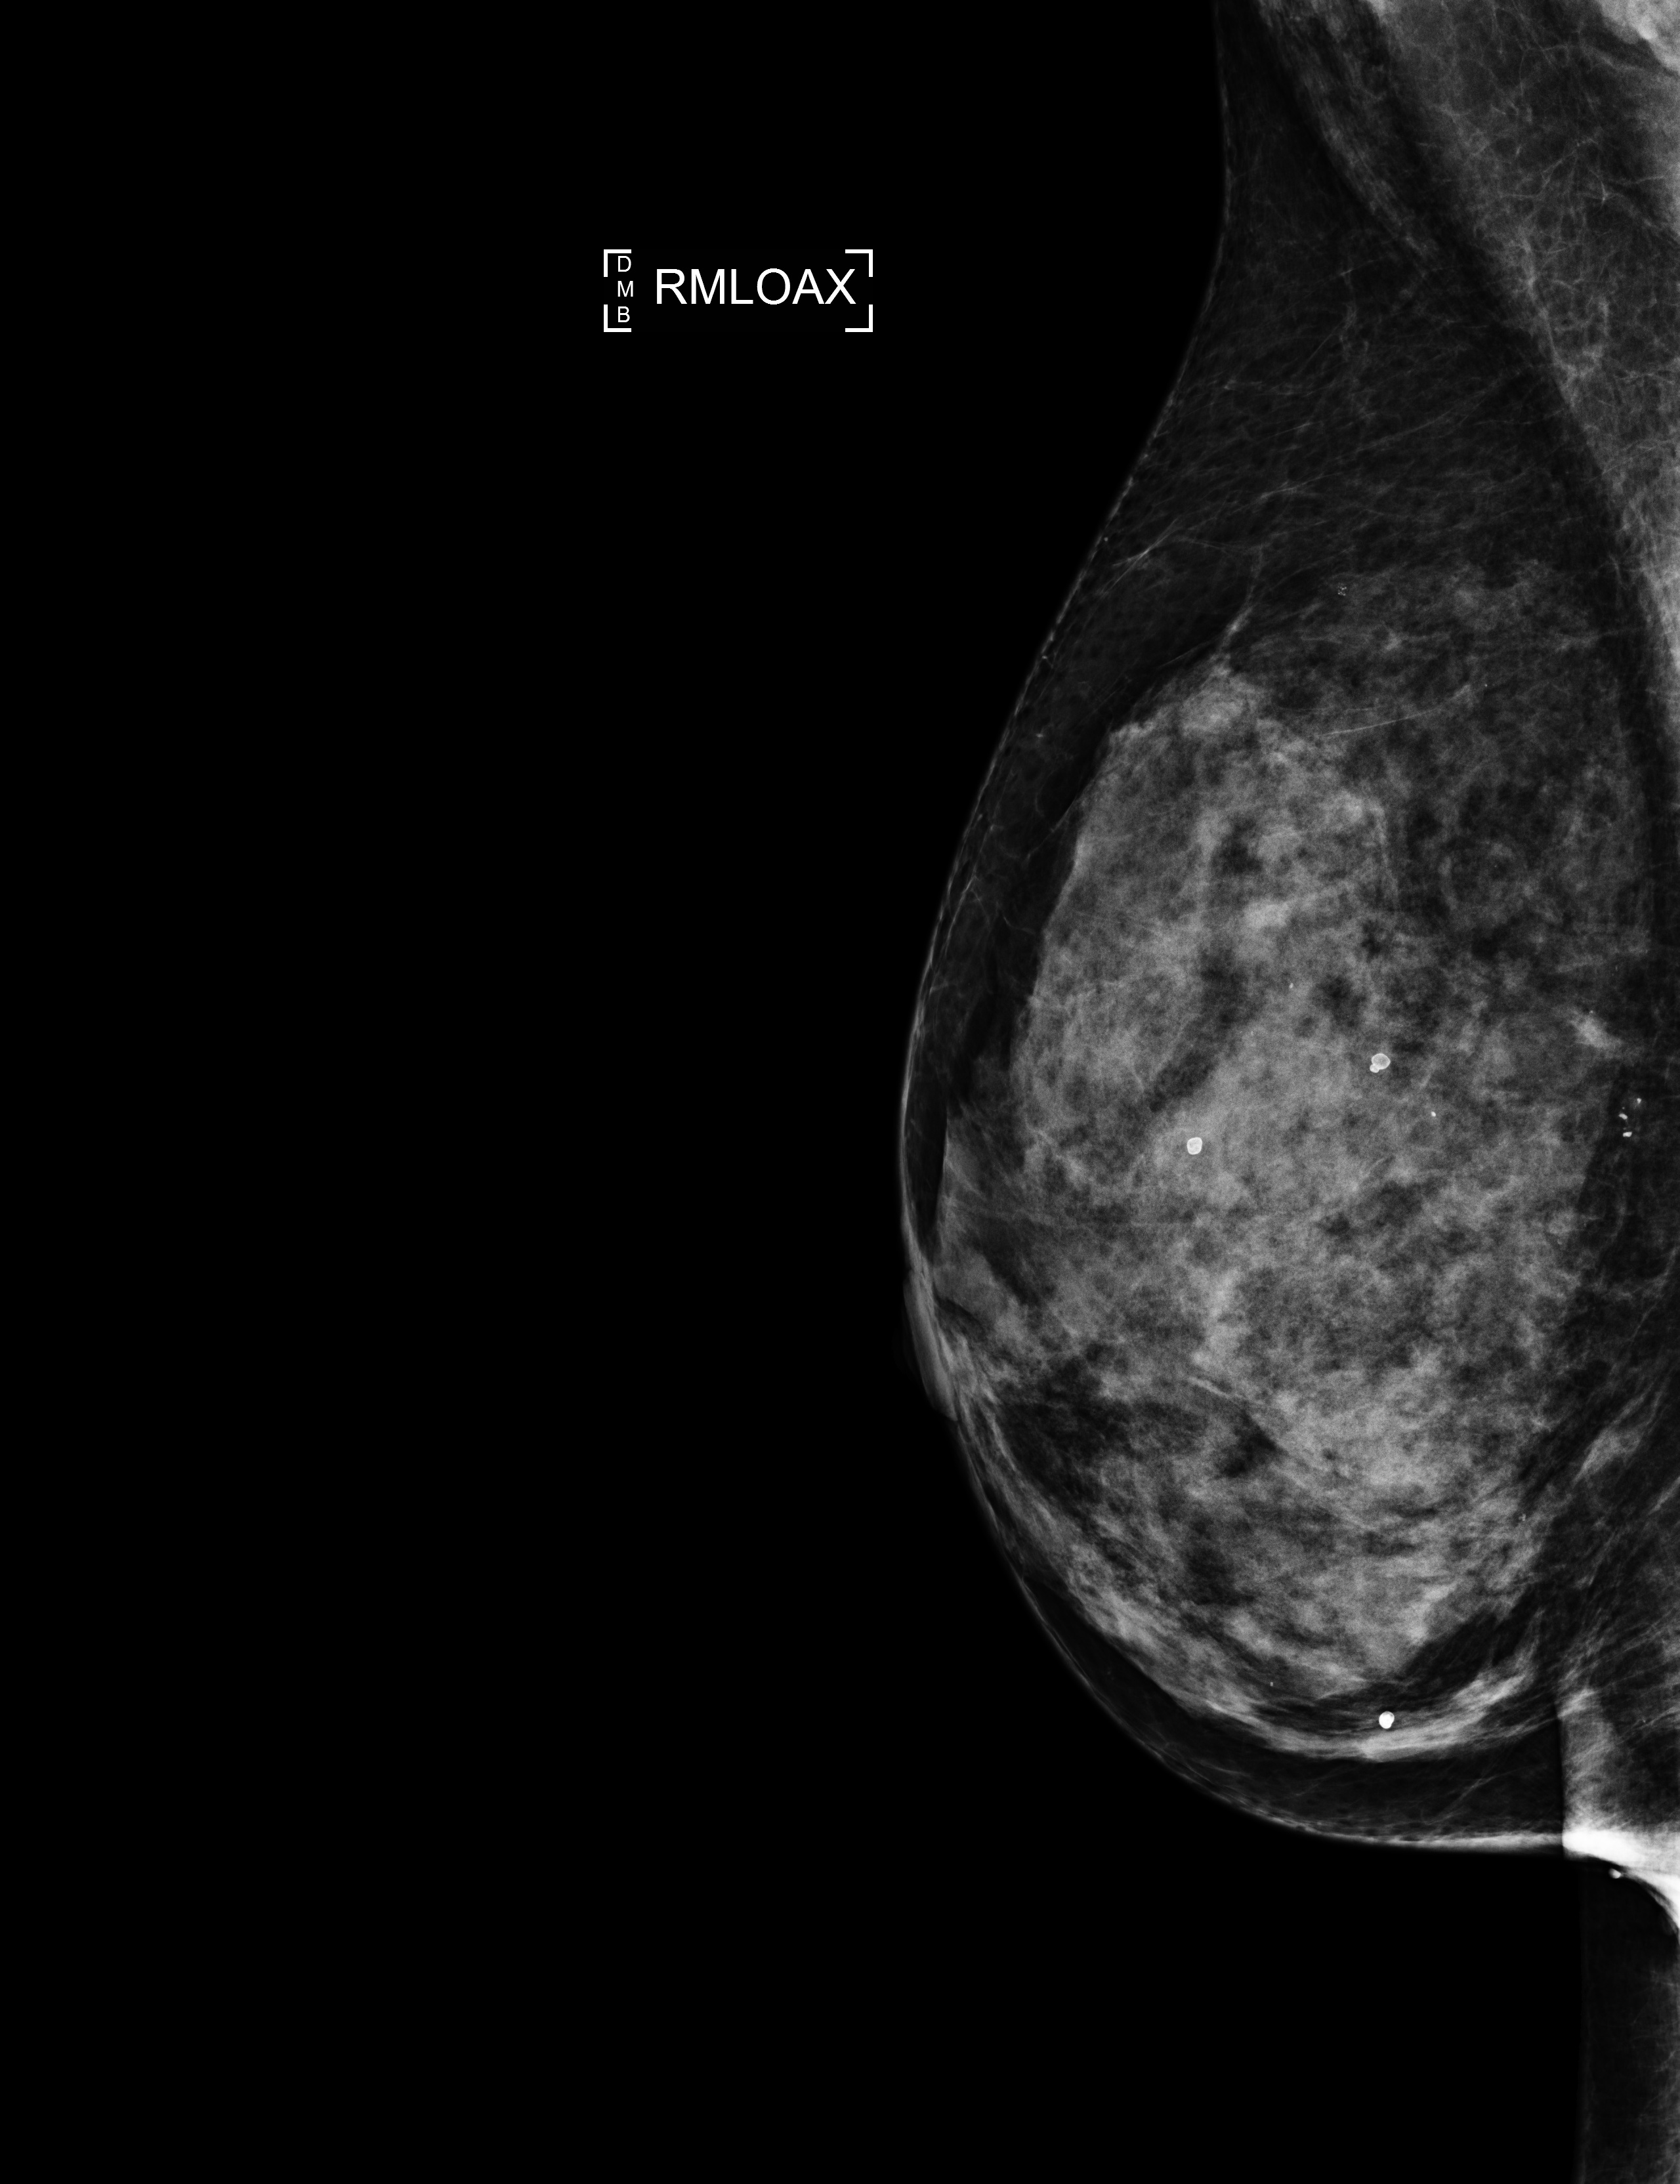
Full-field digital mammogram (FFDM), right breast, medio-lateral oblique projection (axillary tissue), annual screening mammography examination, compressed breast thickness 71 mm, system: Selenia Dimensions. Patient aged 62 years (female).
Breast density at the screening exam (both breasts): extremely dense (BI-RADS density category d). Final BI-RADS category for the screening round (tomosynthesis exam, both breasts): category 1. Recall: no recall after this screen.